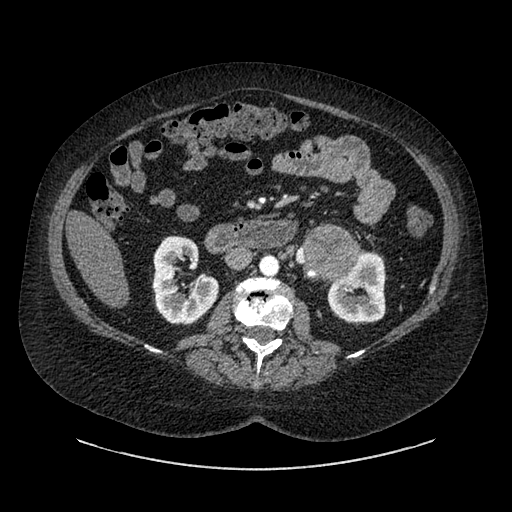
Contrast-enhanced abdominal CT, one axial slice. Position 498 of 769 along the scan axis. Reconstruction kernel SOFT. Intravenous contrast given. Soft-tissue window (W 400 / L 40 HU). 0.62 mm slice thickness. 512 × 512 image matrix, field of view 460 × 460 mm. Female patient, age 61 years. Case-level facts recorded for this patient, not image findings: diagnosis: adrenocortical carcinoma; tumour side: left adrenal; tumour size at pathology: 13 cm; Ki-67 index: 79 %; stage (as recorded): 2.
Outlined on this slice (semi-automatically segmented with operator editing):
- mass: bounding box (x1, y1, x2, y2) in pixels: (309, 230, 357, 277)